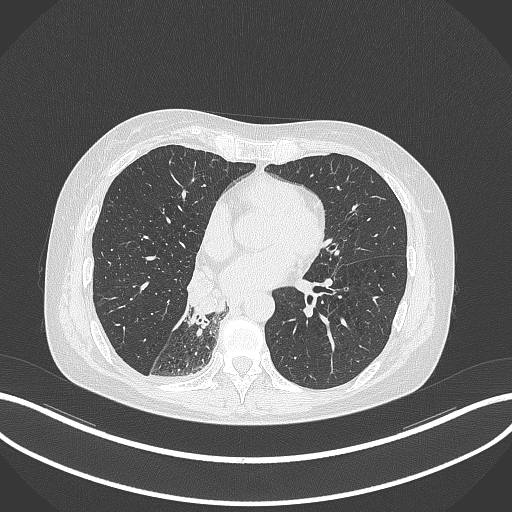
Chest CT, one axial slice. Position 132 of 329 along the scan axis. Reconstruction kernel B70f. 120 kVp. Lung window (W 1500 / L -600 HU). 1 mm slice thickness. 512 × 512 image matrix, field of view 400 × 400 mm. Female patient, age 63 years. From the clinical record (not read from this slice): clinical TNM (as recorded): T1c N0 M0.
Annotated regions visible in this slice (rectangle marked by the reading radiologist):
- lung tumour (recorded histology: adenocarcinoma): bounding box (x1, y1, x2, y2) in pixels: (185, 264, 225, 323)